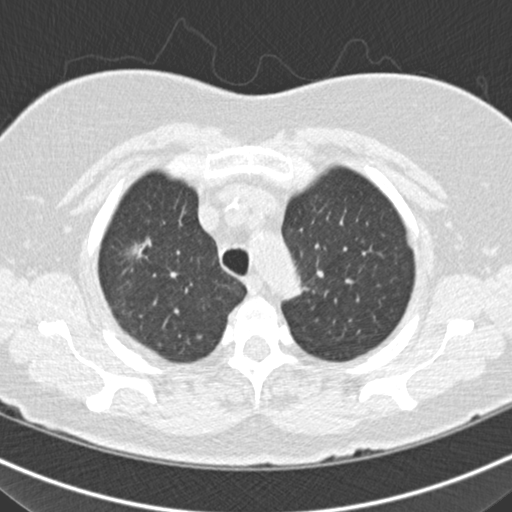
Low-dose screening chest CT, one axial slice. Position 138 of 160 along the scan axis. 120 kVp. Lung window (W 1500 / L -600 HU). 2 mm slice thickness. 512 × 512 image matrix, field of view 316 × 316 mm.
Structures marked on this image (expert manual segmentation):
- lesion 3 (nodule, upper lobe of right lung): bounding box (x1, y1, x2, y2) in pixels: (131, 241, 147, 257)